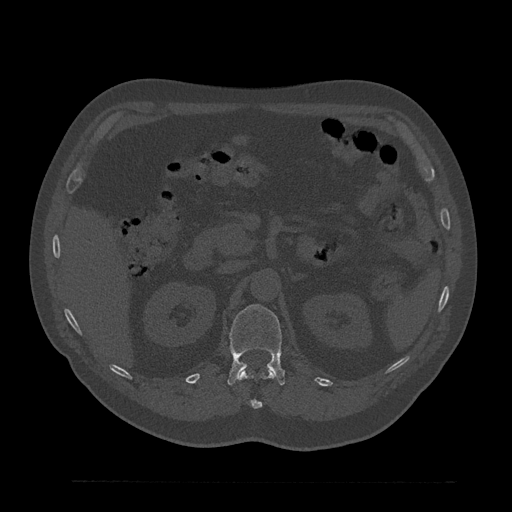
CT including the spine, one axial slice; slice 188 of 797 in the series (ordered by position); 120 kVp; bone window (W 1800 / L 400 HU); 512 × 512 image matrix, field of view 430 × 430 mm. Male patient, age 61 years. From the clinical record (not read from this slice): primary cancer: prostate.
Outlined on this slice (semi-automatically segmented with operator editing):
- L1 vertebra: box from (x=228, y=304) to (x=285, y=386) px
- T12 vertebra: (x=238, y=371)–(x=276, y=409)